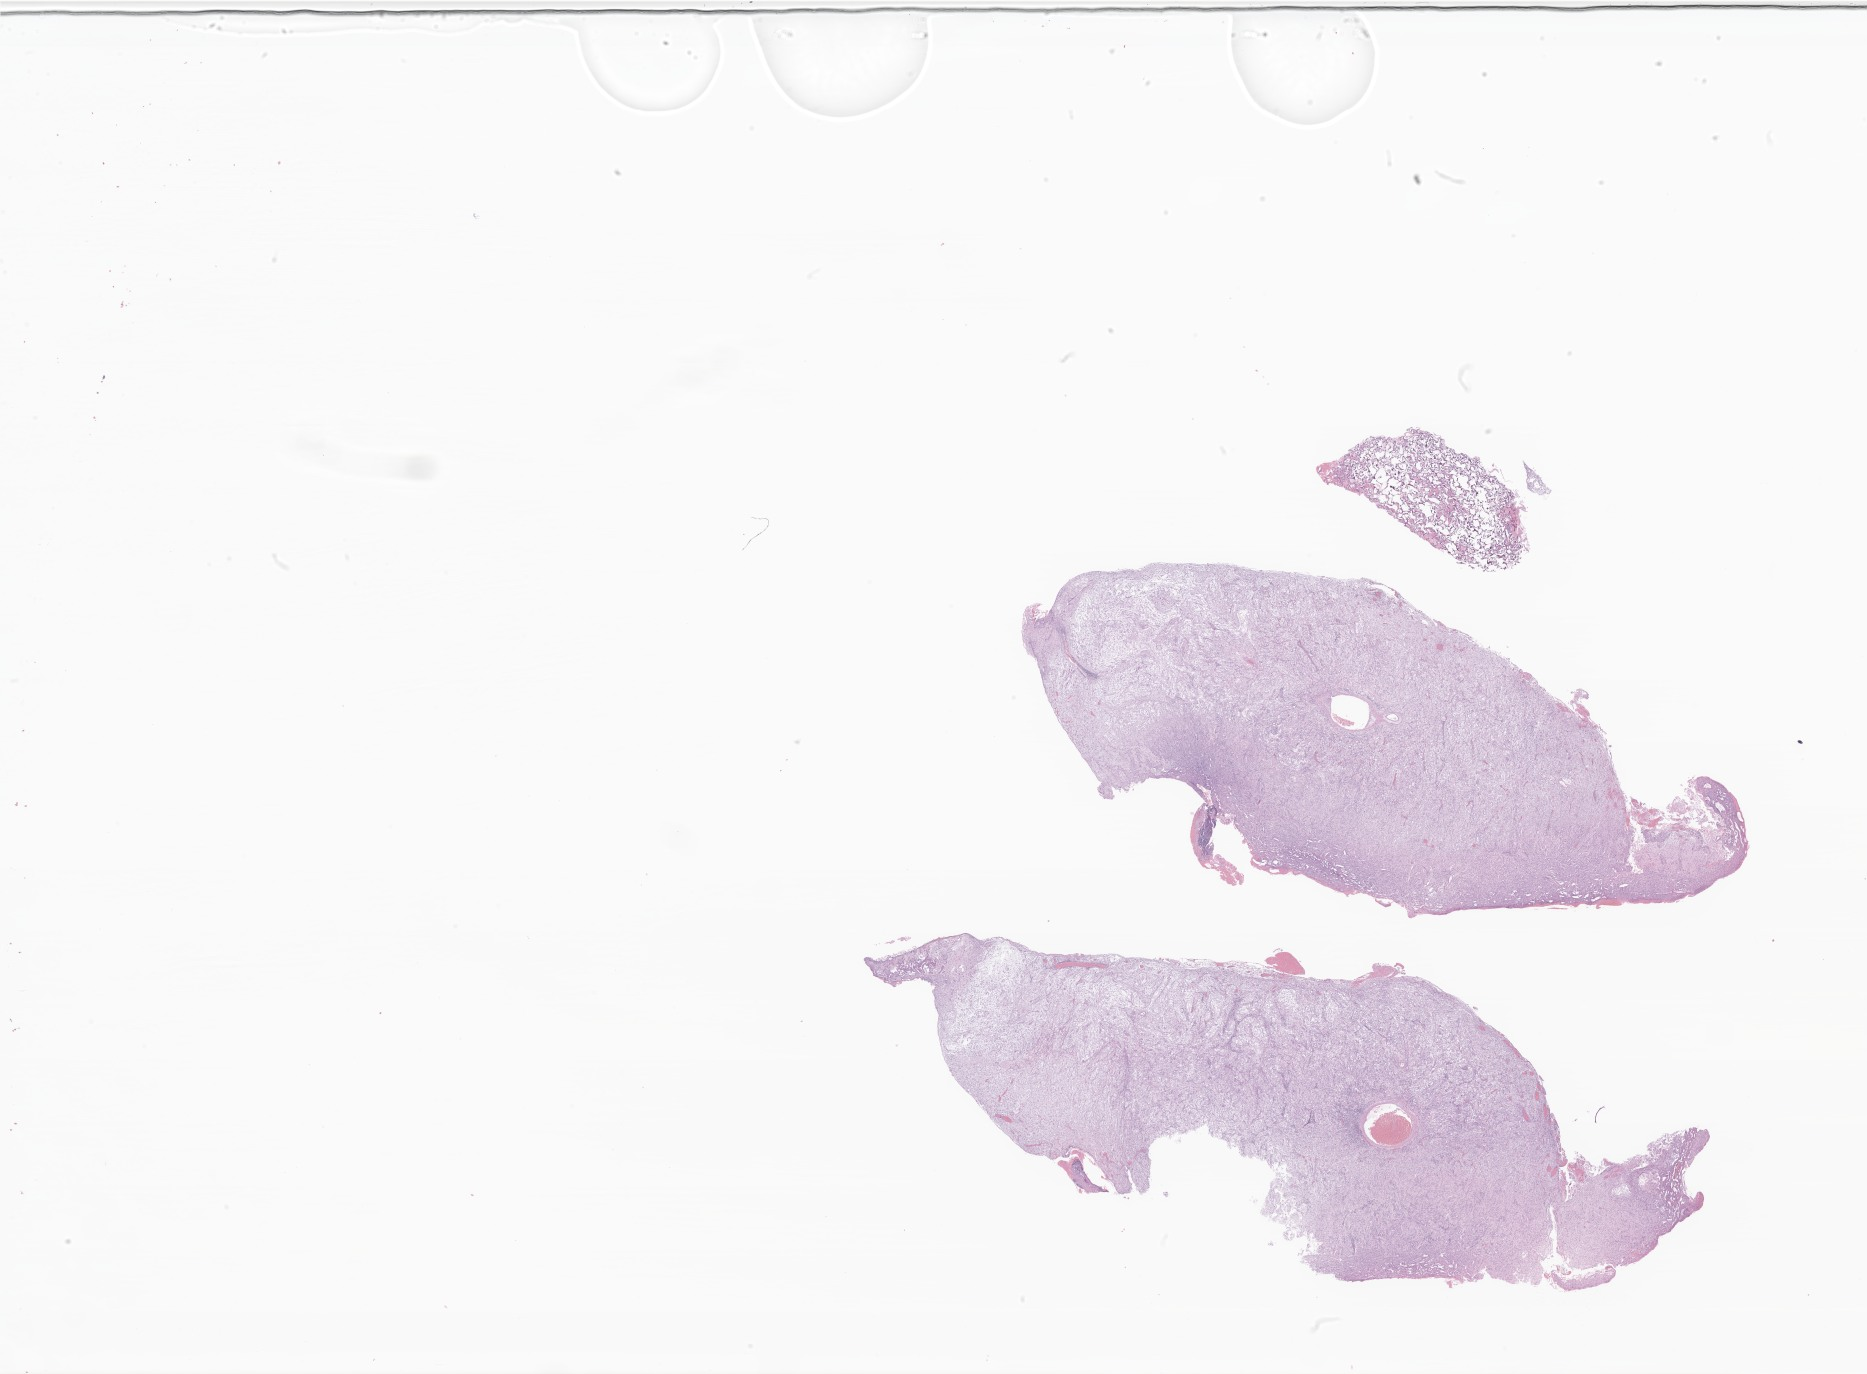
Whole-slide image, hematoxylin and eosin (H&E) stain of tumor tissue from the brain — low-resolution overview of the scanned area, about 31.5 x 23.2 mm. FFPE section. Patient male; age 155 months.
Diagnosis (ICD-O-3 morphology term): Neoplasm, uncertain whether benign or malignant.